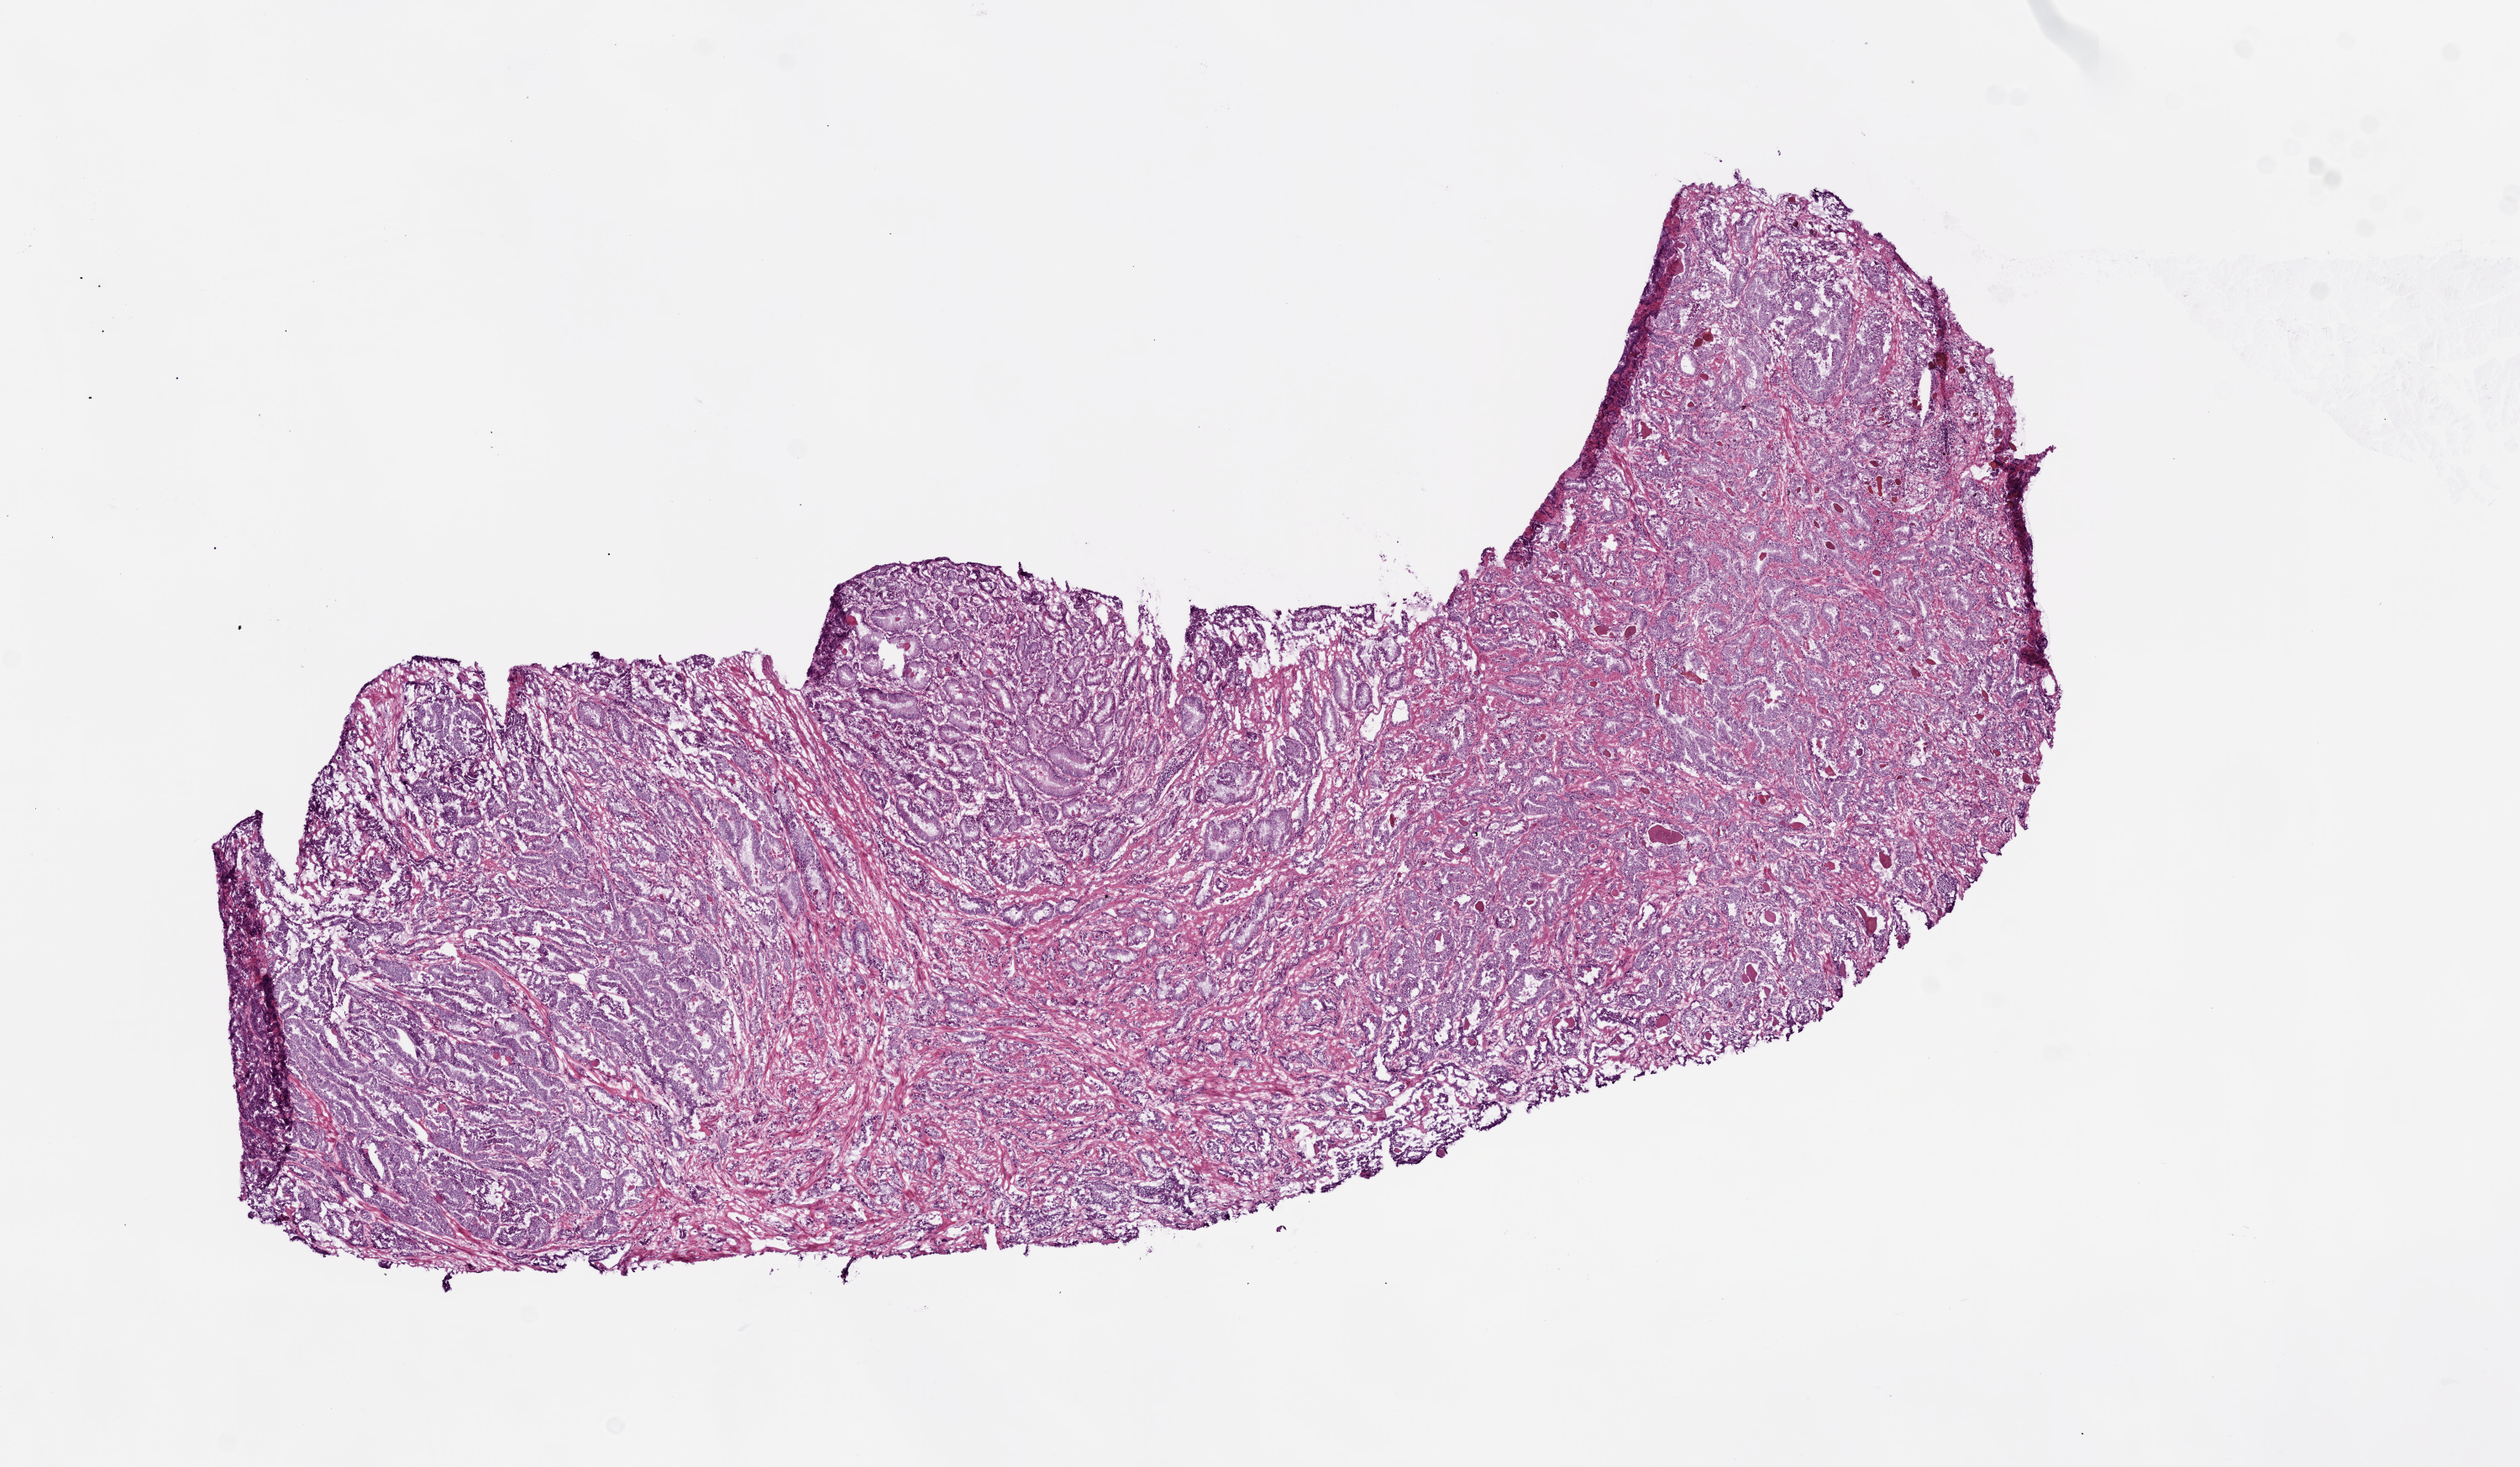
H&E whole-slide image — low-resolution overview of the scanned area, about 12.0 x 7.0 mm (slide scanned at 20x); frozen section; sample: primary tumour, prostate. Male patient; age at initial diagnosis 73 years. Gleason score: 7 (4+3). Pathologist review of this section (percent, as recorded): tumour cells 90%, tumour nuclei 95%, normal cells 1%, stromal cells 9%, necrosis 0%. Infiltration values recorded for this section: lymphocyte infiltration 0%, monocyte infiltration 0%, neutrophil infiltration 0%.
* histologic diagnosis: Acinar cell carcinoma (prostate gland)
* laterality: bilateral